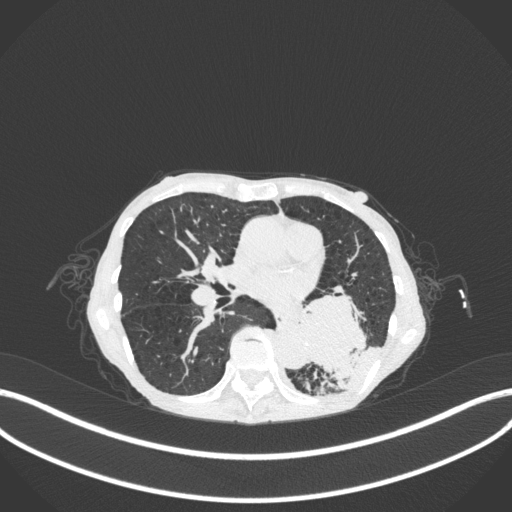
Chest CT, one axial slice. Slice 134 of 347 in the series (ordered by position). 120 kVp. Lung window (W 1500 / L -600 HU). 1 mm slice thickness. 512 × 512 image matrix, field of view 400 × 400 mm. Female patient, age 70 years. Case-level facts recorded for this patient, not image findings: clinical TNM (as recorded): T3 N0 M0.
Outlined on this slice (rectangle marked by the reading radiologist):
- lung tumour (recorded histology: small cell carcinoma): bounding box <292,281,373,381> (left, top, right, bottom; pixels)